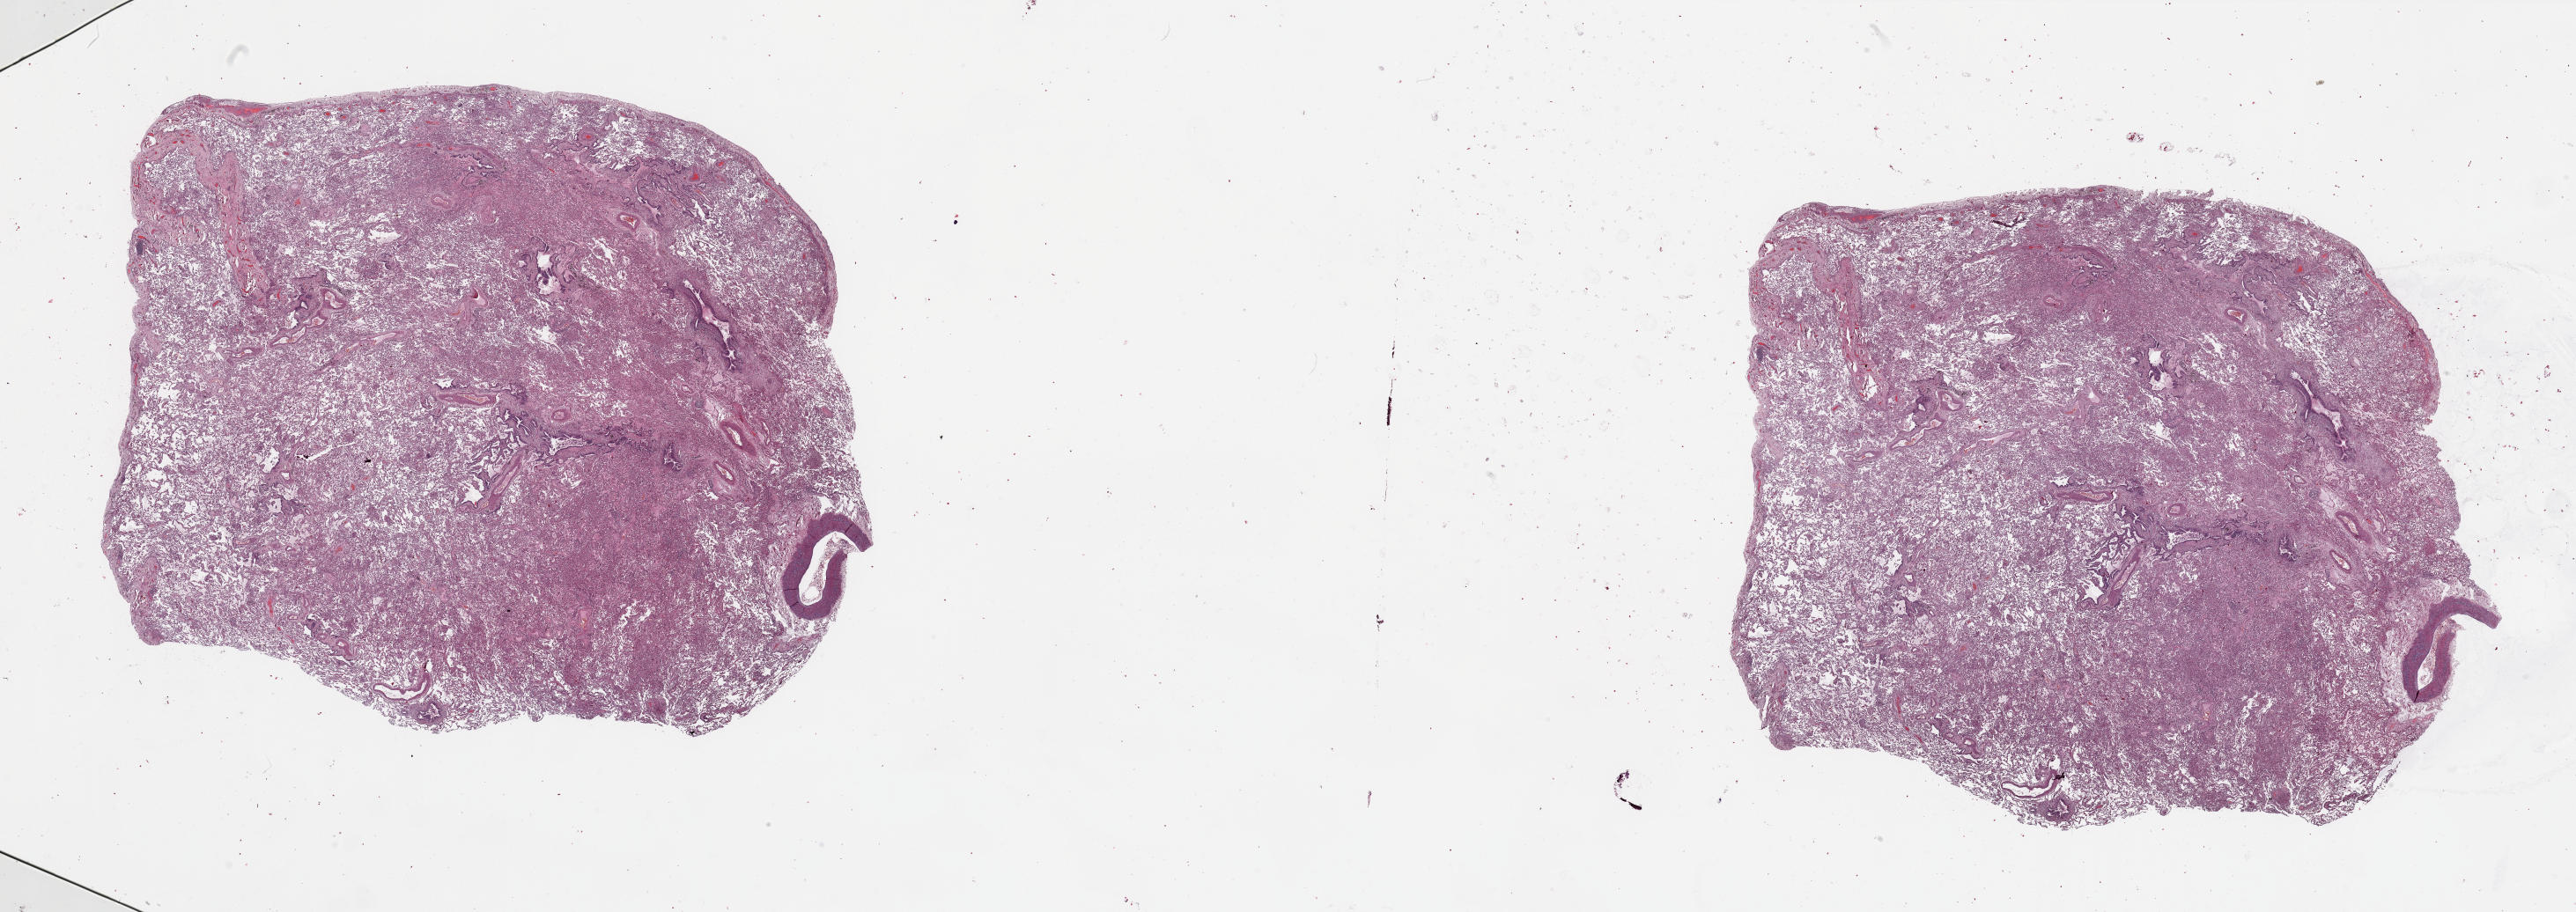
Hematoxylin and eosin (H&E) stained whole-slide image, whole scanned area (about 46.3 x 16.4 mm, slide scanned at 20x) shown as a low-resolution overview; normal (non-tumour) tissue sample, sampled site: lung. Male, 74 y/o.
This section: normal (non-tumour) tissue from the same patient. Patient diagnosis: Squamous cell carcinoma, NOS.